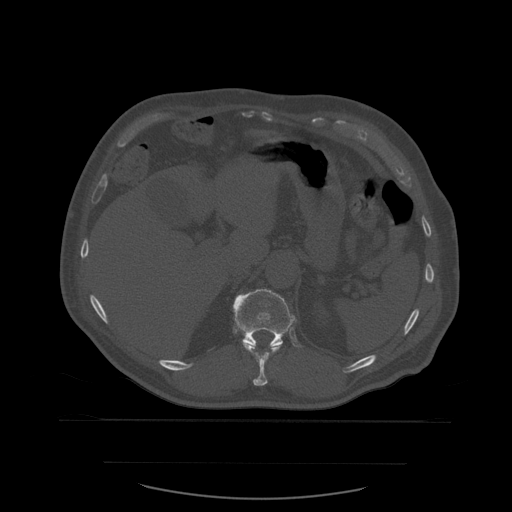
CT including the spine, one axial slice; position 283 of 590 along the scan axis; bone window (W 1800 / L 400 HU); 512 × 512 image matrix, field of view 479 × 479 mm. Patient age 71 years. From the clinical record (not read from this slice): primary cancer: lung.
Annotated regions visible in this slice (semi-automatic segmentation, software-assisted and operator-edited):
- T11 vertebra: bounding box <244,344,281,386> (left, top, right, bottom; pixels)
- T12 vertebra: <233,289,297,349>